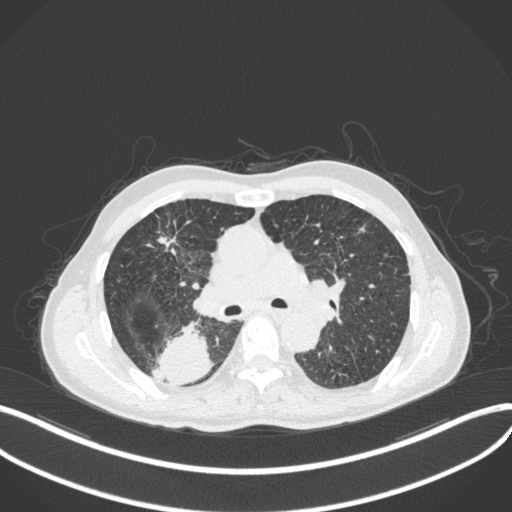
Chest CT, one axial slice; lung window (W 1500 / L -600 HU); 512 × 512 image matrix. Patient: male, 79 years. Case-level facts recorded for this patient, not image findings: clinical TNM (as recorded): T3 N0 M0.
Annotated regions visible in this slice (bounding box drawn by a radiologist):
- lung tumour (recorded histology: adenocarcinoma): bounding box [x1, y1, x2, y2] px = [151, 317, 216, 387]